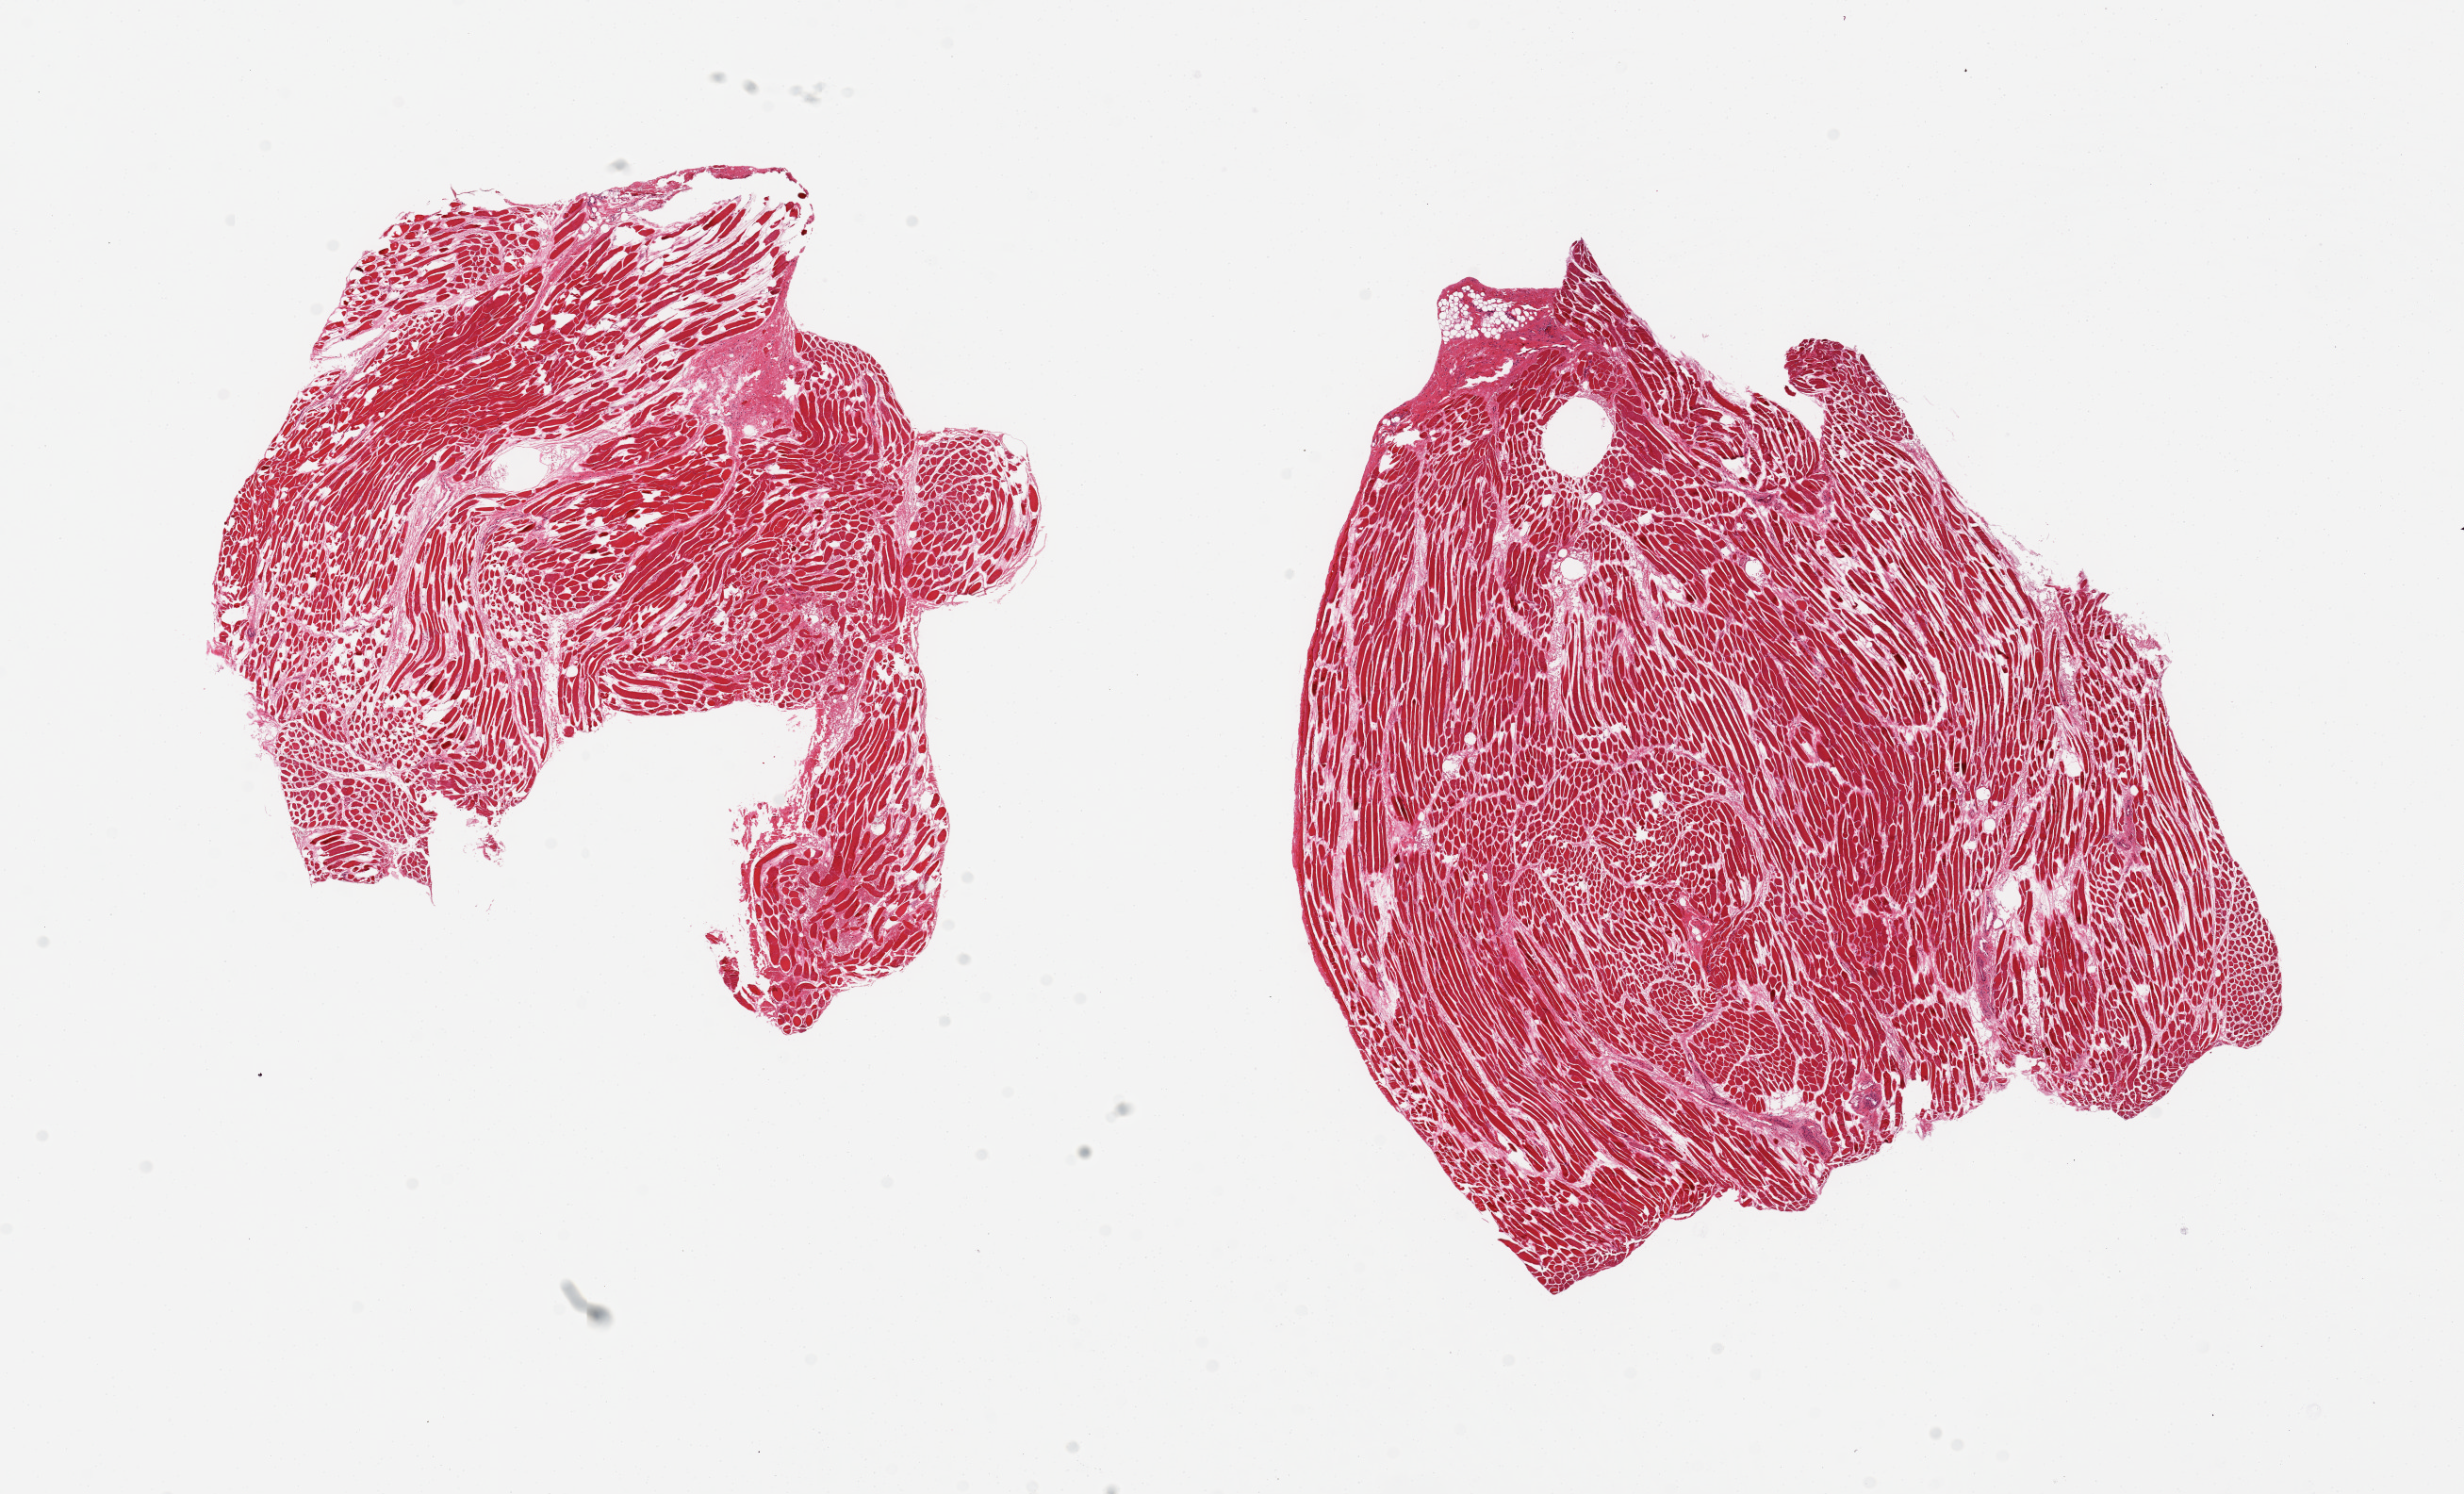
Digitized H&E-stained section, brightfield, a low-resolution overview of the entire scanned area, about 20.7 x 12.5 mm; PAXgene-fixed paraffin-embedded (PFPE) section; sampled site (target tissue): thyroid; donor tissue sample. Donor: male.
Reviewer comment on this tissue sample: 2 pieces, 7x7 & 9x8mm; no thyroid parenchyma, strap/skeletal muscle only.